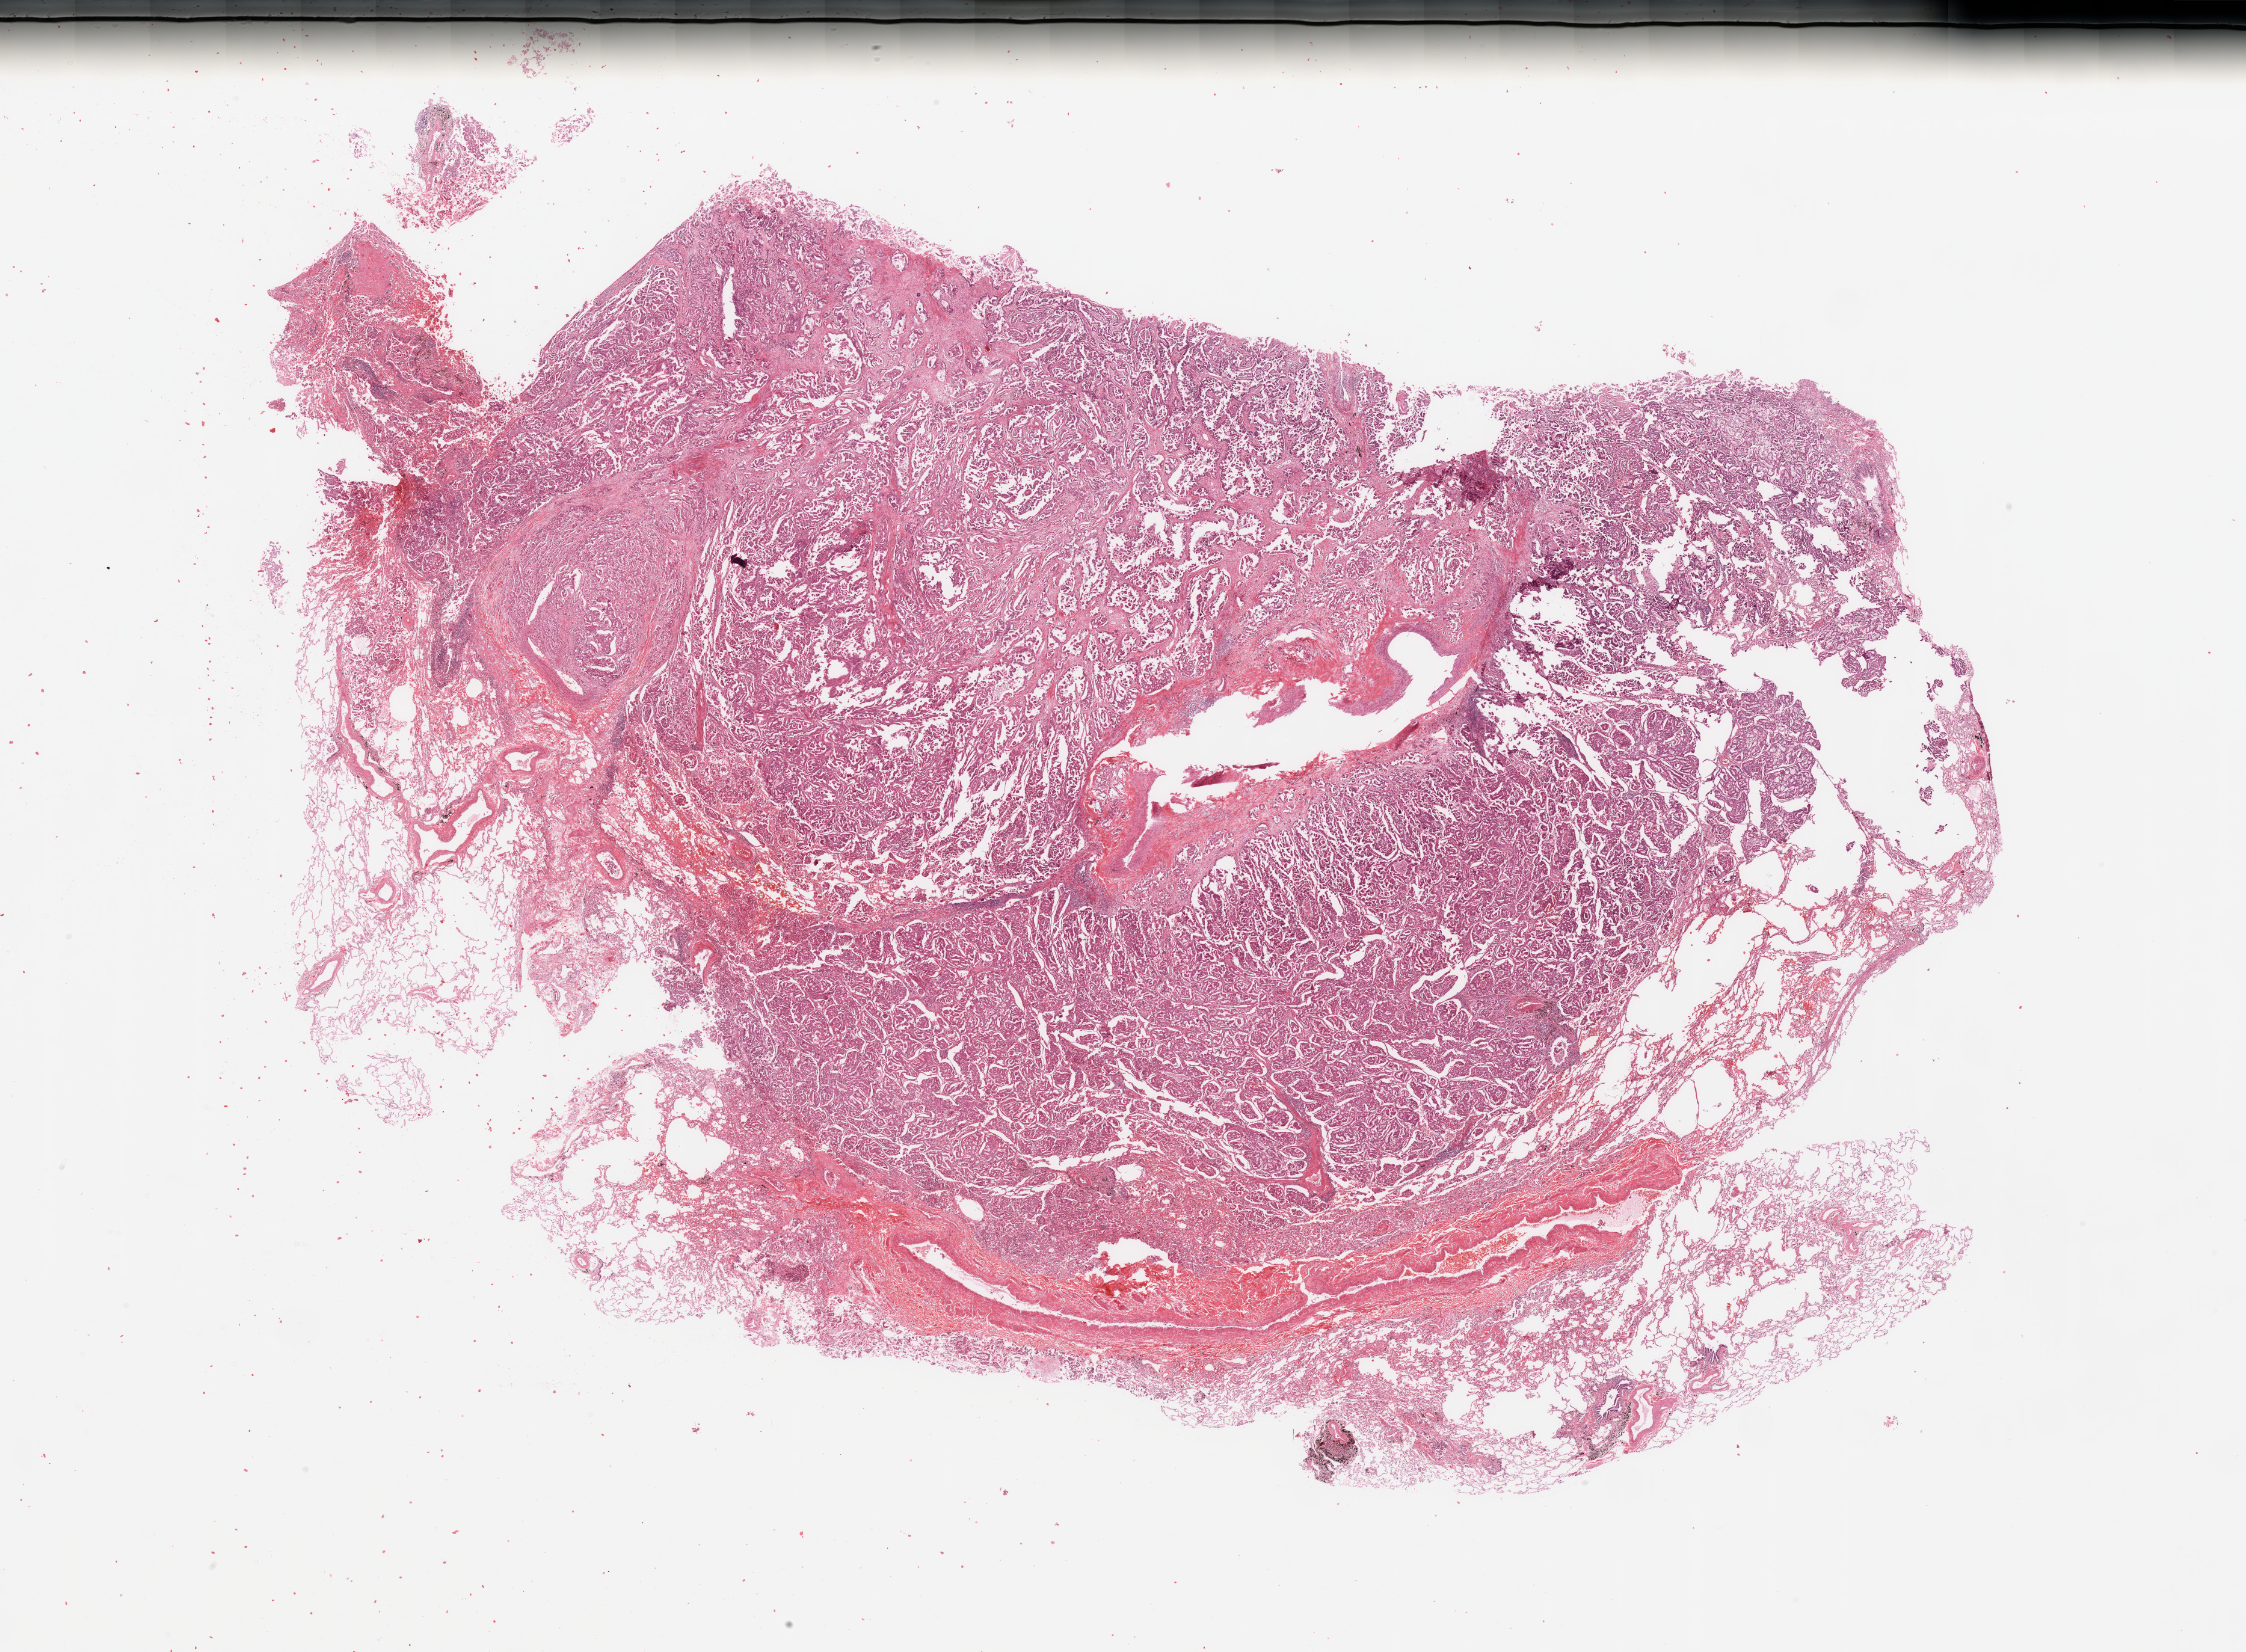
Digitized H&E-stained tissue section (whole slide), low-resolution overview of the scanned area, about 29.5 x 21.7 mm (from a 20x scan), tumour tissue sample, lung. Male, 55 y/o. Histologic grade: G2 (moderately differentiated).
Histologic diagnosis: Adenocarcinoma, NOS. AJCC pathologic stage: IIIA.